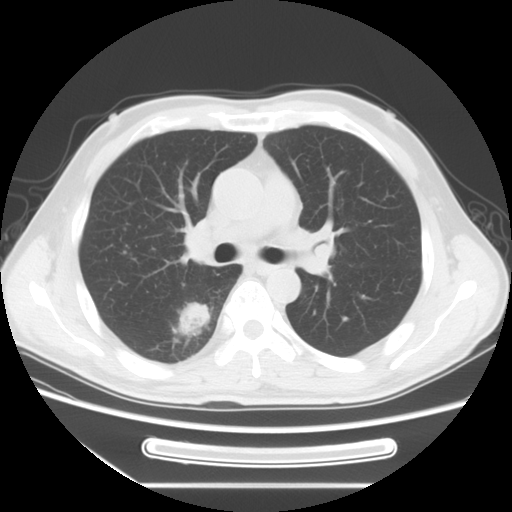
Chest CT, one axial slice. Position 45 of 71 along the scan axis. 120 kVp. Lung window (W 1500 / L -600 HU). 5 mm slice thickness. 512 × 512 image matrix, field of view 366 × 366 mm. Patient: male, 51 years. Case-level facts recorded for this patient, not image findings: clinical TNM (as recorded): T1c N3 M0.
Annotated regions visible in this slice (rectangle marked by the reading radiologist):
- lung tumour (recorded histology: adenocarcinoma): bounding box [x1, y1, x2, y2] px = [290, 210, 342, 285]